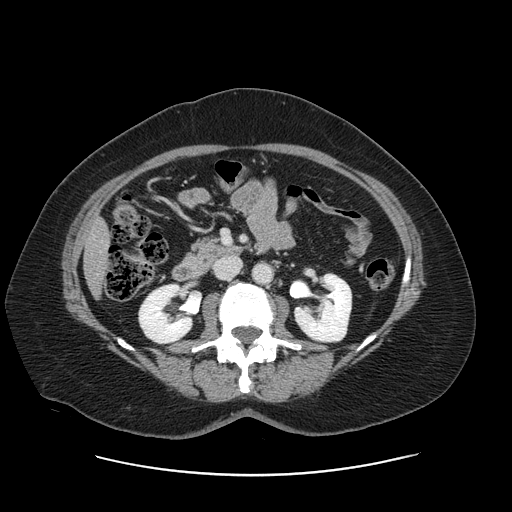
Contrast-enhanced abdominal CT, one axial slice. Position 49 of 161 along the scan axis. 120 kVp. Intravenous contrast given. Soft-tissue window (W 400 / L 40 HU). 2.5 mm slice thickness. 512 × 512 image matrix, field of view 398 × 398 mm. Female patient, age 62 years. From the clinical record (not read from this slice): diagnosis: colorectal cancer liver metastases, imaged before liver resection.
Outlined on this slice (manually delineated by an expert):
- liver: bounding box [x1, y1, x2, y2] px = [86, 220, 109, 293]